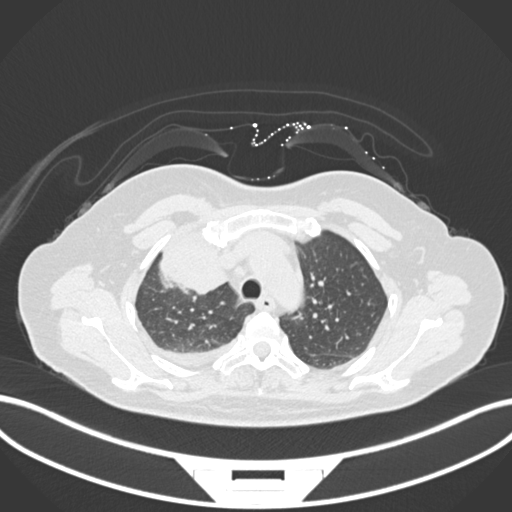
Chest CT, one axial slice; slice 124 of 172 in the series (ordered by position); reconstruction kernel B30f; 120 kVp; lung window (W 1500 / L -600 HU); 1 mm slice thickness; 512 × 512 image matrix. Female patient, age 52 years. Case-level facts recorded for this patient, not image findings: clinical TNM (as recorded): T3 N1 M1.
Outlined on this slice (bounding box drawn by a radiologist):
- lung tumour (recorded histology: adenocarcinoma): box from (x=156, y=226) to (x=230, y=293) px